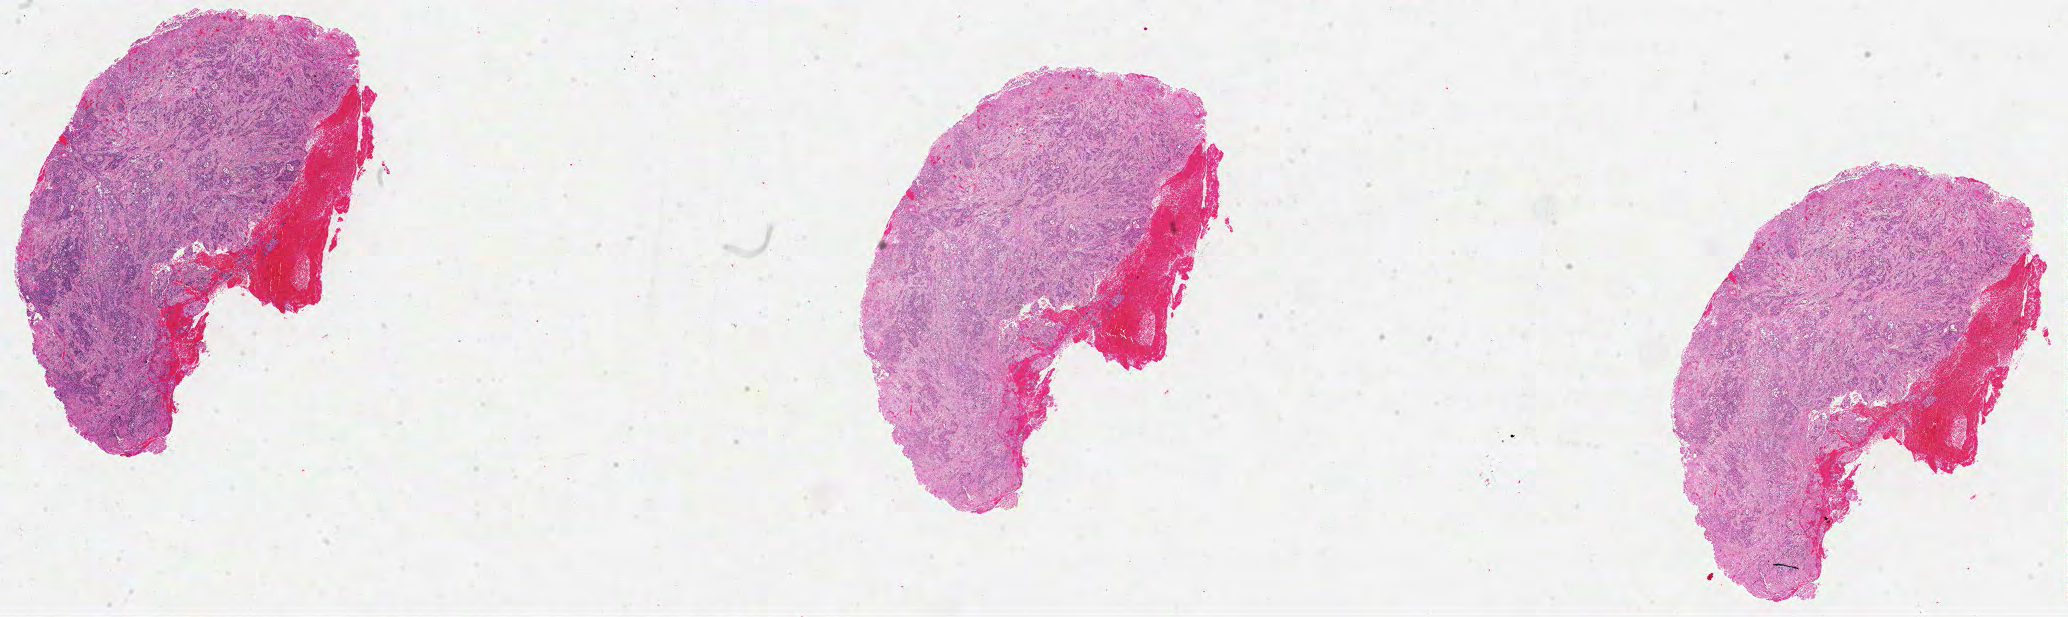
H&E whole-slide image, whole scanned area (about 33.4 x 10.0 mm, from a 40x scan) shown as a low-resolution overview, formalin-fixed paraffin-embedded (FFPE) diagnostic section, primary tumour sample from the head and neck. Patient: male, age at initial diagnosis 69 years. Histologic grade: G3 (poorly differentiated).
Diagnosis: Squamous cell carcinoma, NOS (tongue, NOS). AJCC pathologic stage: IVA (6th edition).